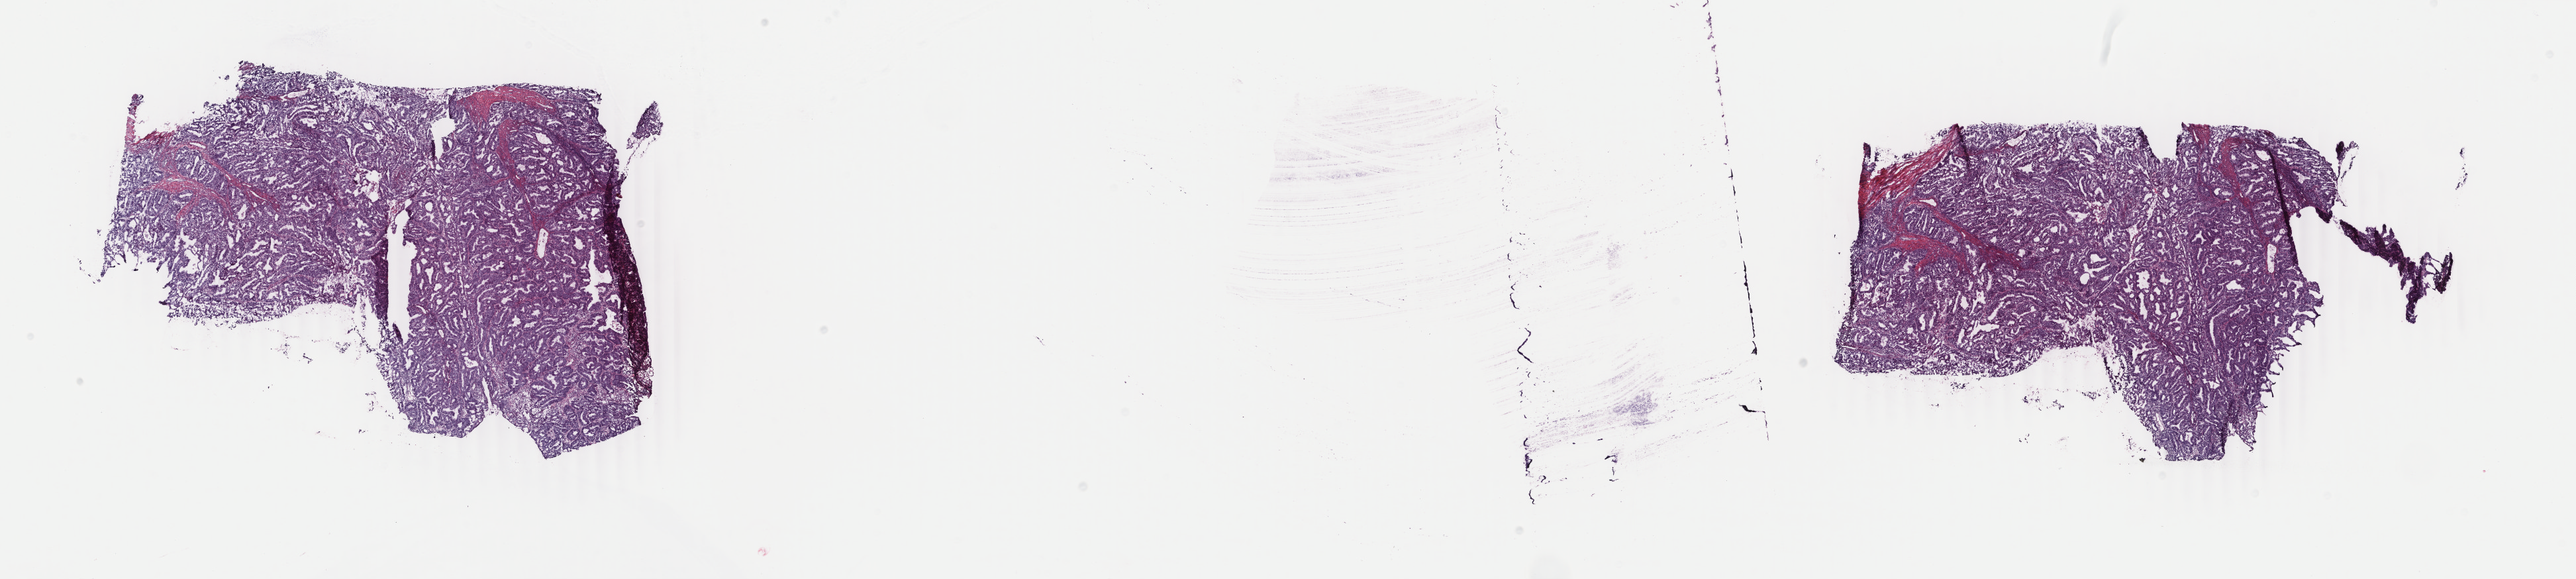
Hematoxylin and eosin (H&E) stained whole-slide image, shown as a low-resolution overview of the whole scanned area (about 30.9 x 7.0 mm). Frozen section. Uterus, primary tumour sample. Female patient; age at initial diagnosis 51 years. Histologic grade: G2 (moderately differentiated). Composition of this section per pathologist review: tumour cells 95%, tumour nuclei 95%, normal cells 0%, stromal cells 5%, necrosis 0%. Inflammatory infiltration, as recorded: lymphocyte infiltration 0%, monocyte infiltration 0%, neutrophil infiltration 0%.
FIGO stage: IA. Diagnosis: Endometrioid adenocarcinoma, NOS (endometrium).